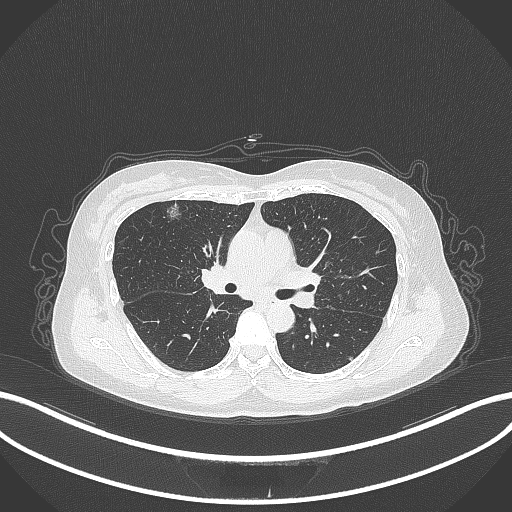
Chest CT, one axial slice; position 195 of 315 along the scan axis; lung window (W 1500 / L -600 HU); 1 mm slice thickness; 512 × 512 image matrix, field of view 400 × 400 mm. Patient: female, 61 years. Case-level facts recorded for this patient, not image findings: clinical TNM (as recorded): T1b N0 M0; histopathological grade: G1.
Annotated regions visible in this slice (bounding box drawn by a radiologist):
- lung tumour (recorded histology: adenocarcinoma): bounding box <159,197,186,224> (left, top, right, bottom; pixels)